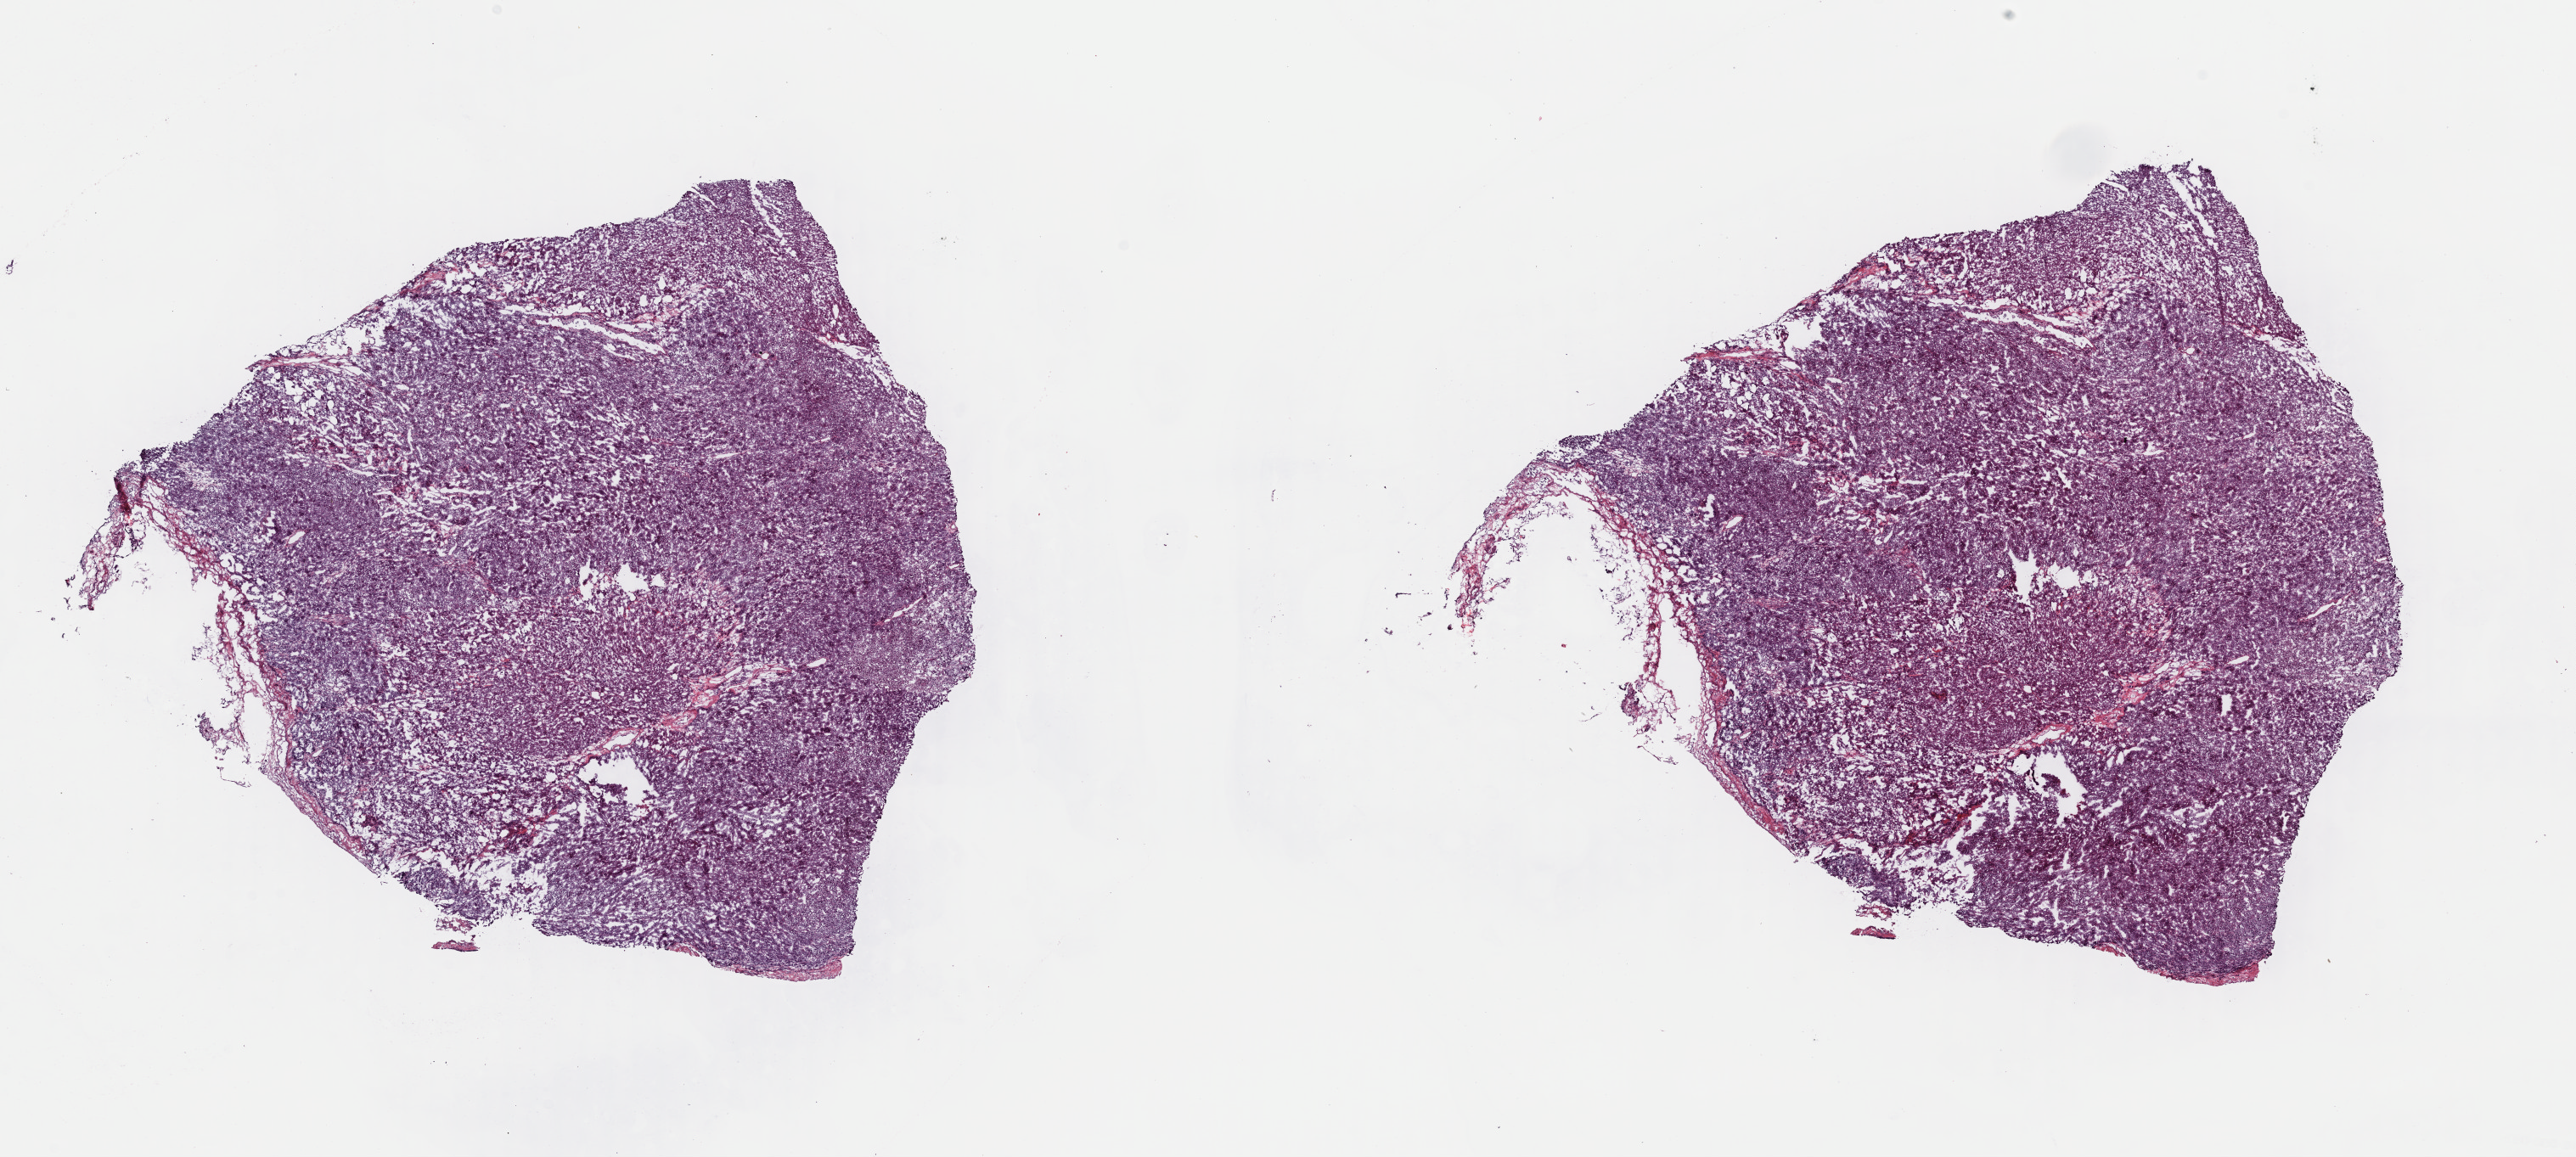
H&E-stained whole-slide image, whole scanned area (about 23.9 x 10.8 mm) shown as a low-resolution overview; frozen section; primary tumour sample from the adrenal cortex. Female patient; age at initial diagnosis 77 years. Pathologist review of this section (percent, as recorded): tumour cells 90%, tumour nuclei 95%, normal cells 0%, stromal cells 5%, necrosis 5%. Inflammatory infiltration, as recorded: lymphocyte infiltration 0%, monocyte infiltration 0%, neutrophil infiltration 0%.
* histologic diagnosis: Adrenal cortical carcinoma (cortex of adrenal gland)